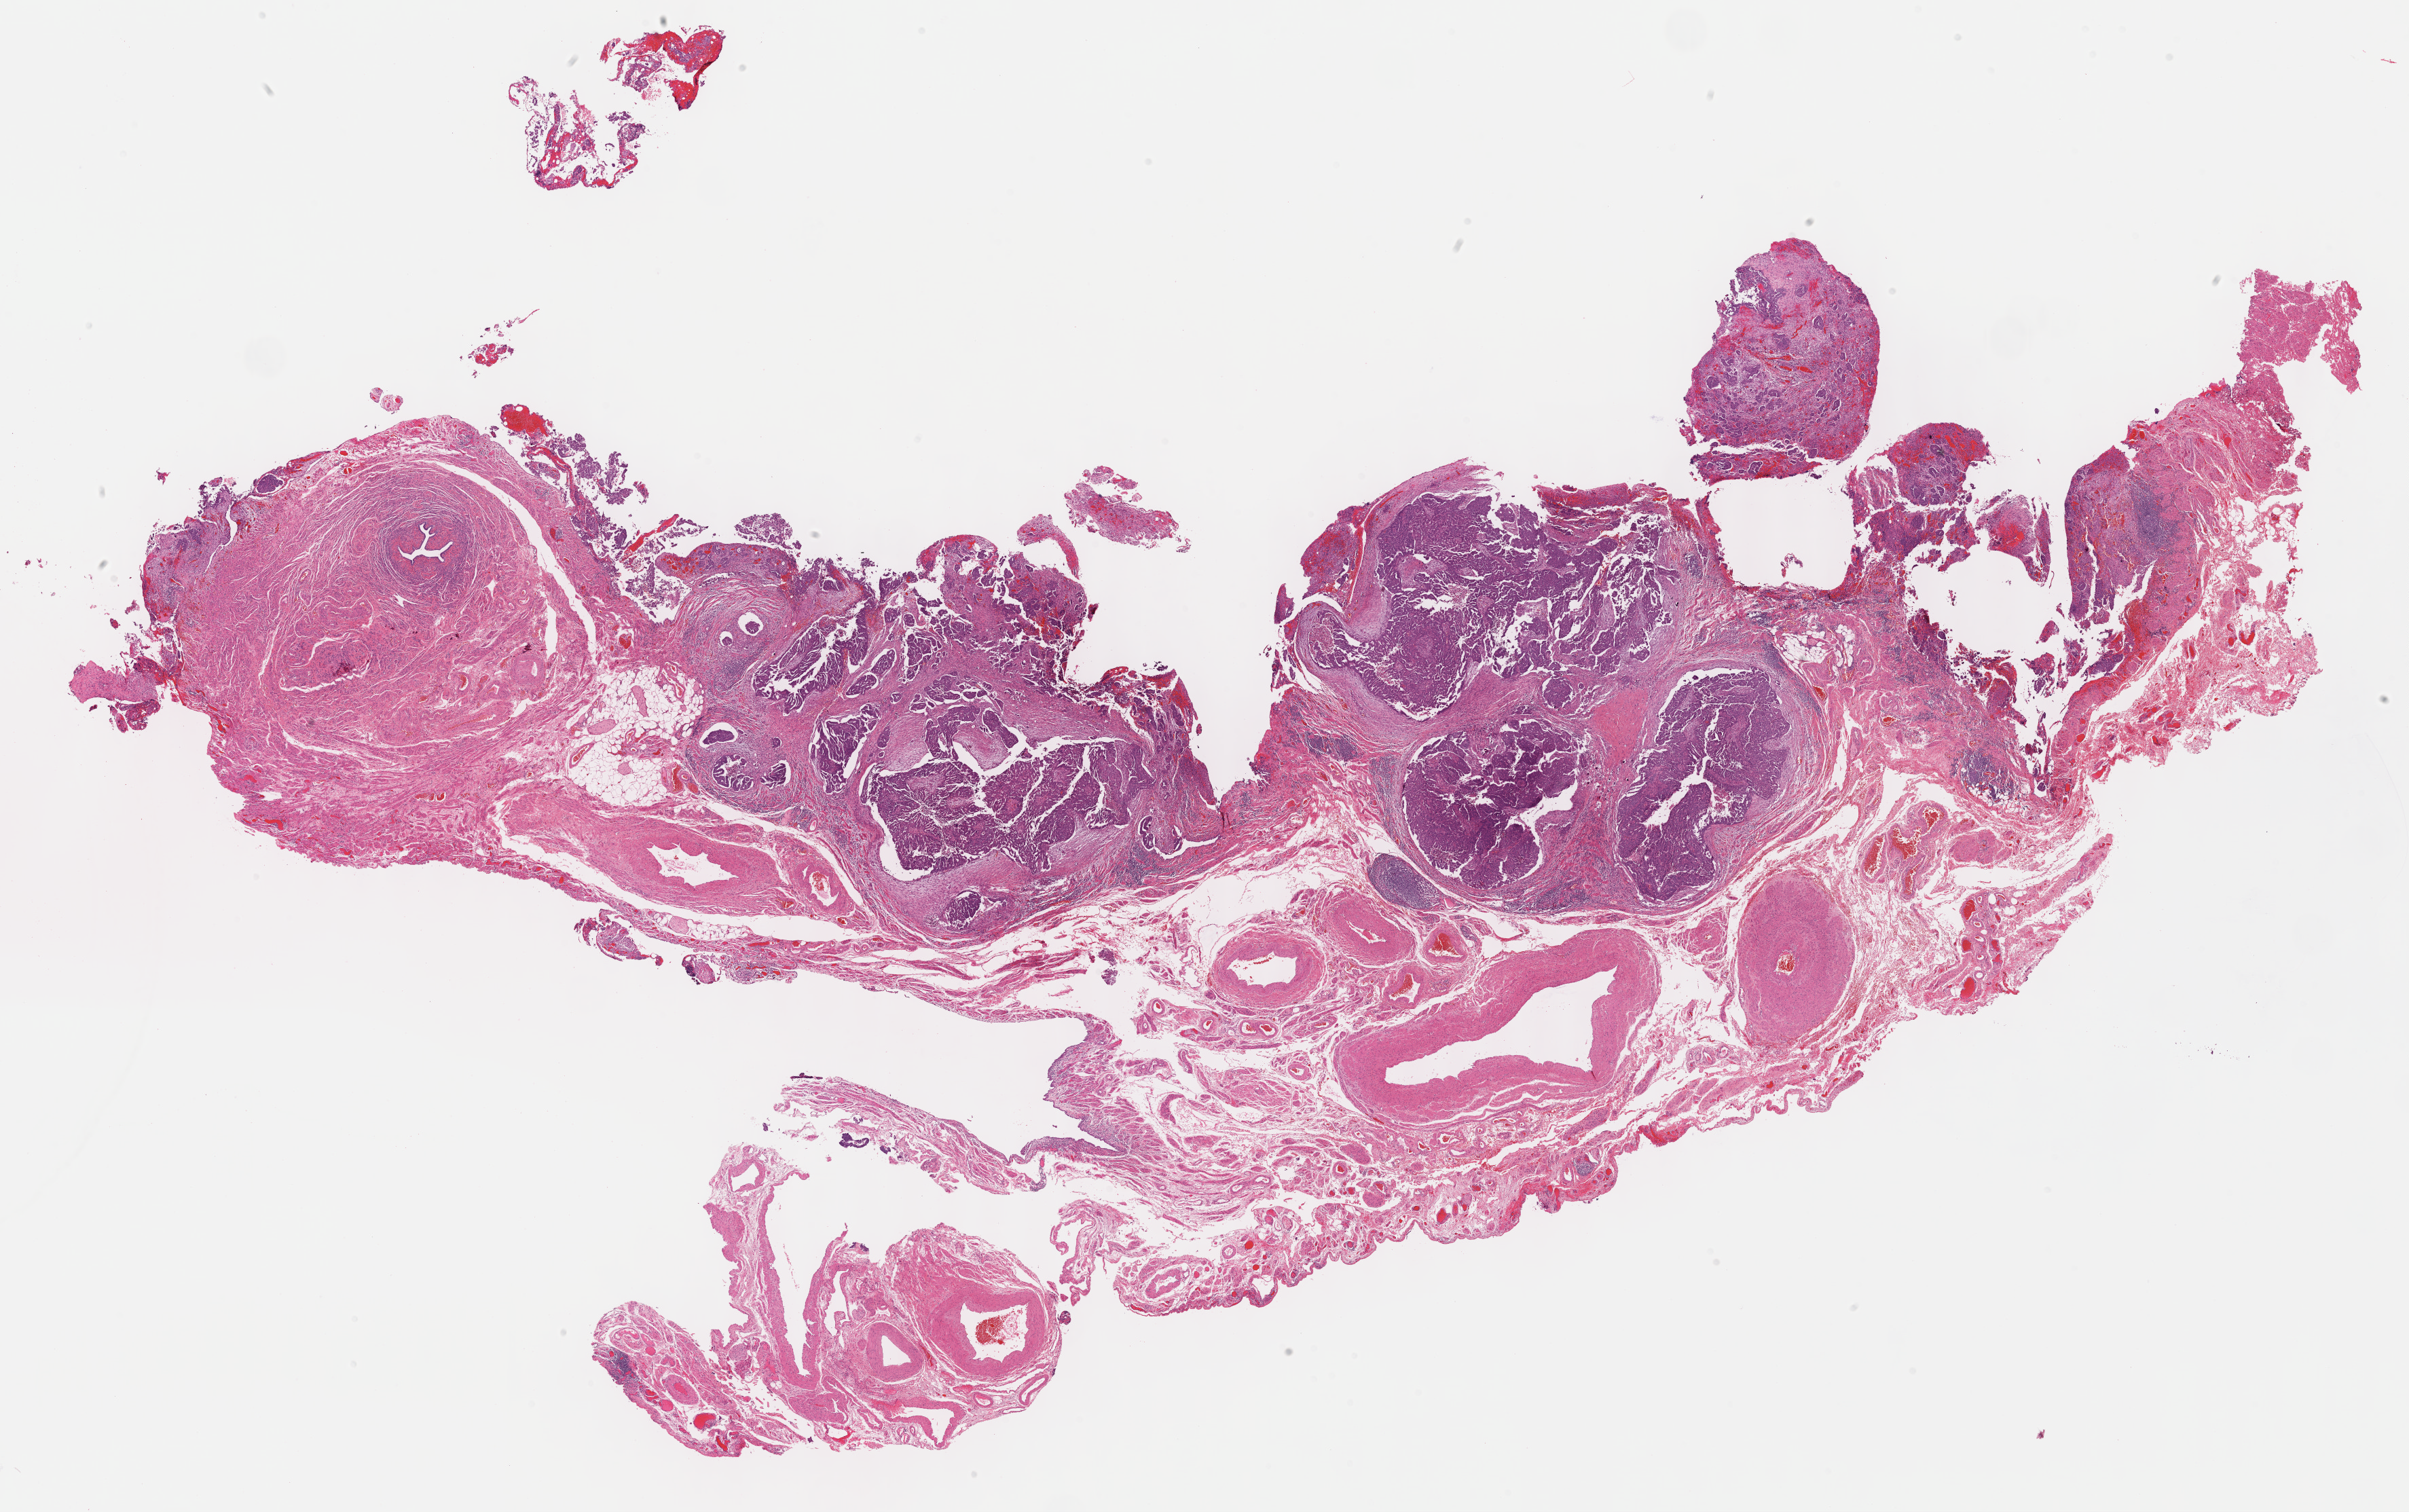
Digitized H&E-stained tissue section (whole slide), whole scanned area (about 28.7 x 18.0 mm) shown as a low-resolution overview, formalin-fixed paraffin-embedded (FFPE) diagnostic section, sample: primary tumour, ovary. Female patient; age at initial diagnosis 66 years. Histologic grade: G3 (poorly differentiated).
Laterality: bilateral. Pathologic diagnosis: Serous cystadenocarcinoma, NOS. FIGO stage: IIIC.